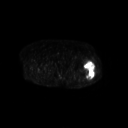
FDG PET of an extremity soft-tissue mass (from a PET/CT study), one axial slice. Position 251 of 267 along the scan axis. 128 × 128 image matrix, field of view 700 × 700 mm. Female patient, age 62 years. Case-level facts recorded for this patient, not image findings: histological type: undifferentiated – high grade; grade: high; site of the primary tumour: left thigh.
Structures marked on this image (expert contour drawn on MRI and transferred to this co-registered scan by the dataset authors):
- gross tumour volume including surrounding oedema: bounding box <84,61,95,79> (left, top, right, bottom; pixels)
- gross tumour volume (mass): <84,62,95,79>